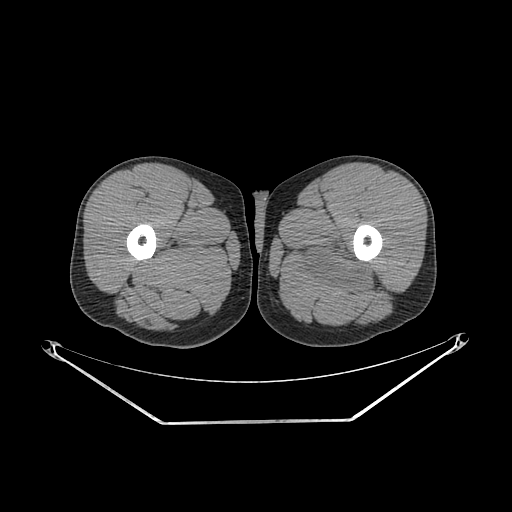
CT of an extremity soft-tissue mass (from a PET/CT study), one axial slice. Slice 247 of 267 in the series (ordered by position). 140 kVp. Soft-tissue window (W 400 / L 40 HU). 3.75 mm slice thickness. 512 × 512 image matrix. Male patient. Case-level facts recorded for this patient, not image findings: histological type: extraskeletal osteosarcoma; grade: high; site of the primary tumour: left adductur.
Outlined on this slice (expert contour drawn on MRI and transferred to this co-registered scan by the dataset authors):
- gross tumour volume (mass): bounding box [x1, y1, x2, y2] px = [290, 235, 378, 295]